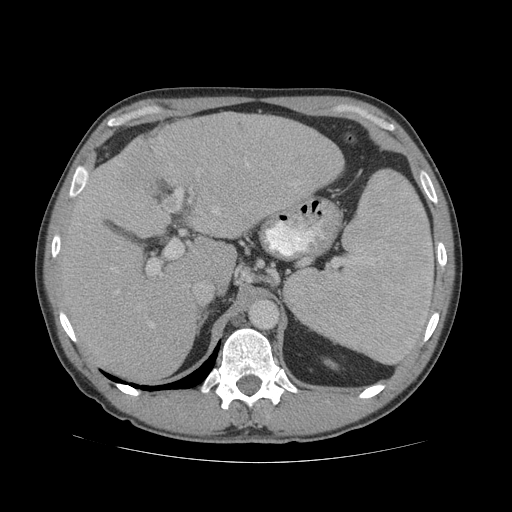
Contrast-enhanced abdominal CT (liver protocol), one axial slice; slice 43 of 81 in the series (ordered by position); 140 kVp; soft-tissue window (W 400 / L 40 HU); 512 × 512 image matrix. Case-level facts recorded for this patient, not image findings: diagnosis: hepatocellular carcinoma (patient treated with transarterial chemoembolisation; whether this scan precedes or follows treatment is not stated here); TNM stage (as recorded): Stage-IVB; Child-Pugh class: B; tumour differentiation: well differentiated; tumour nodularity: multinodular.
Outlined on this slice (semi-automatic segmentation, software-assisted and operator-edited):
- liver parenchyma outside the tumour (the mass and vessels are separate outlines, so this box may not span the whole liver): bounding box (x1, y1, x2, y2) in pixels: (56, 112, 344, 382)
- mass: (116, 138, 180, 196)
- liver vessels: (112, 163, 296, 327)